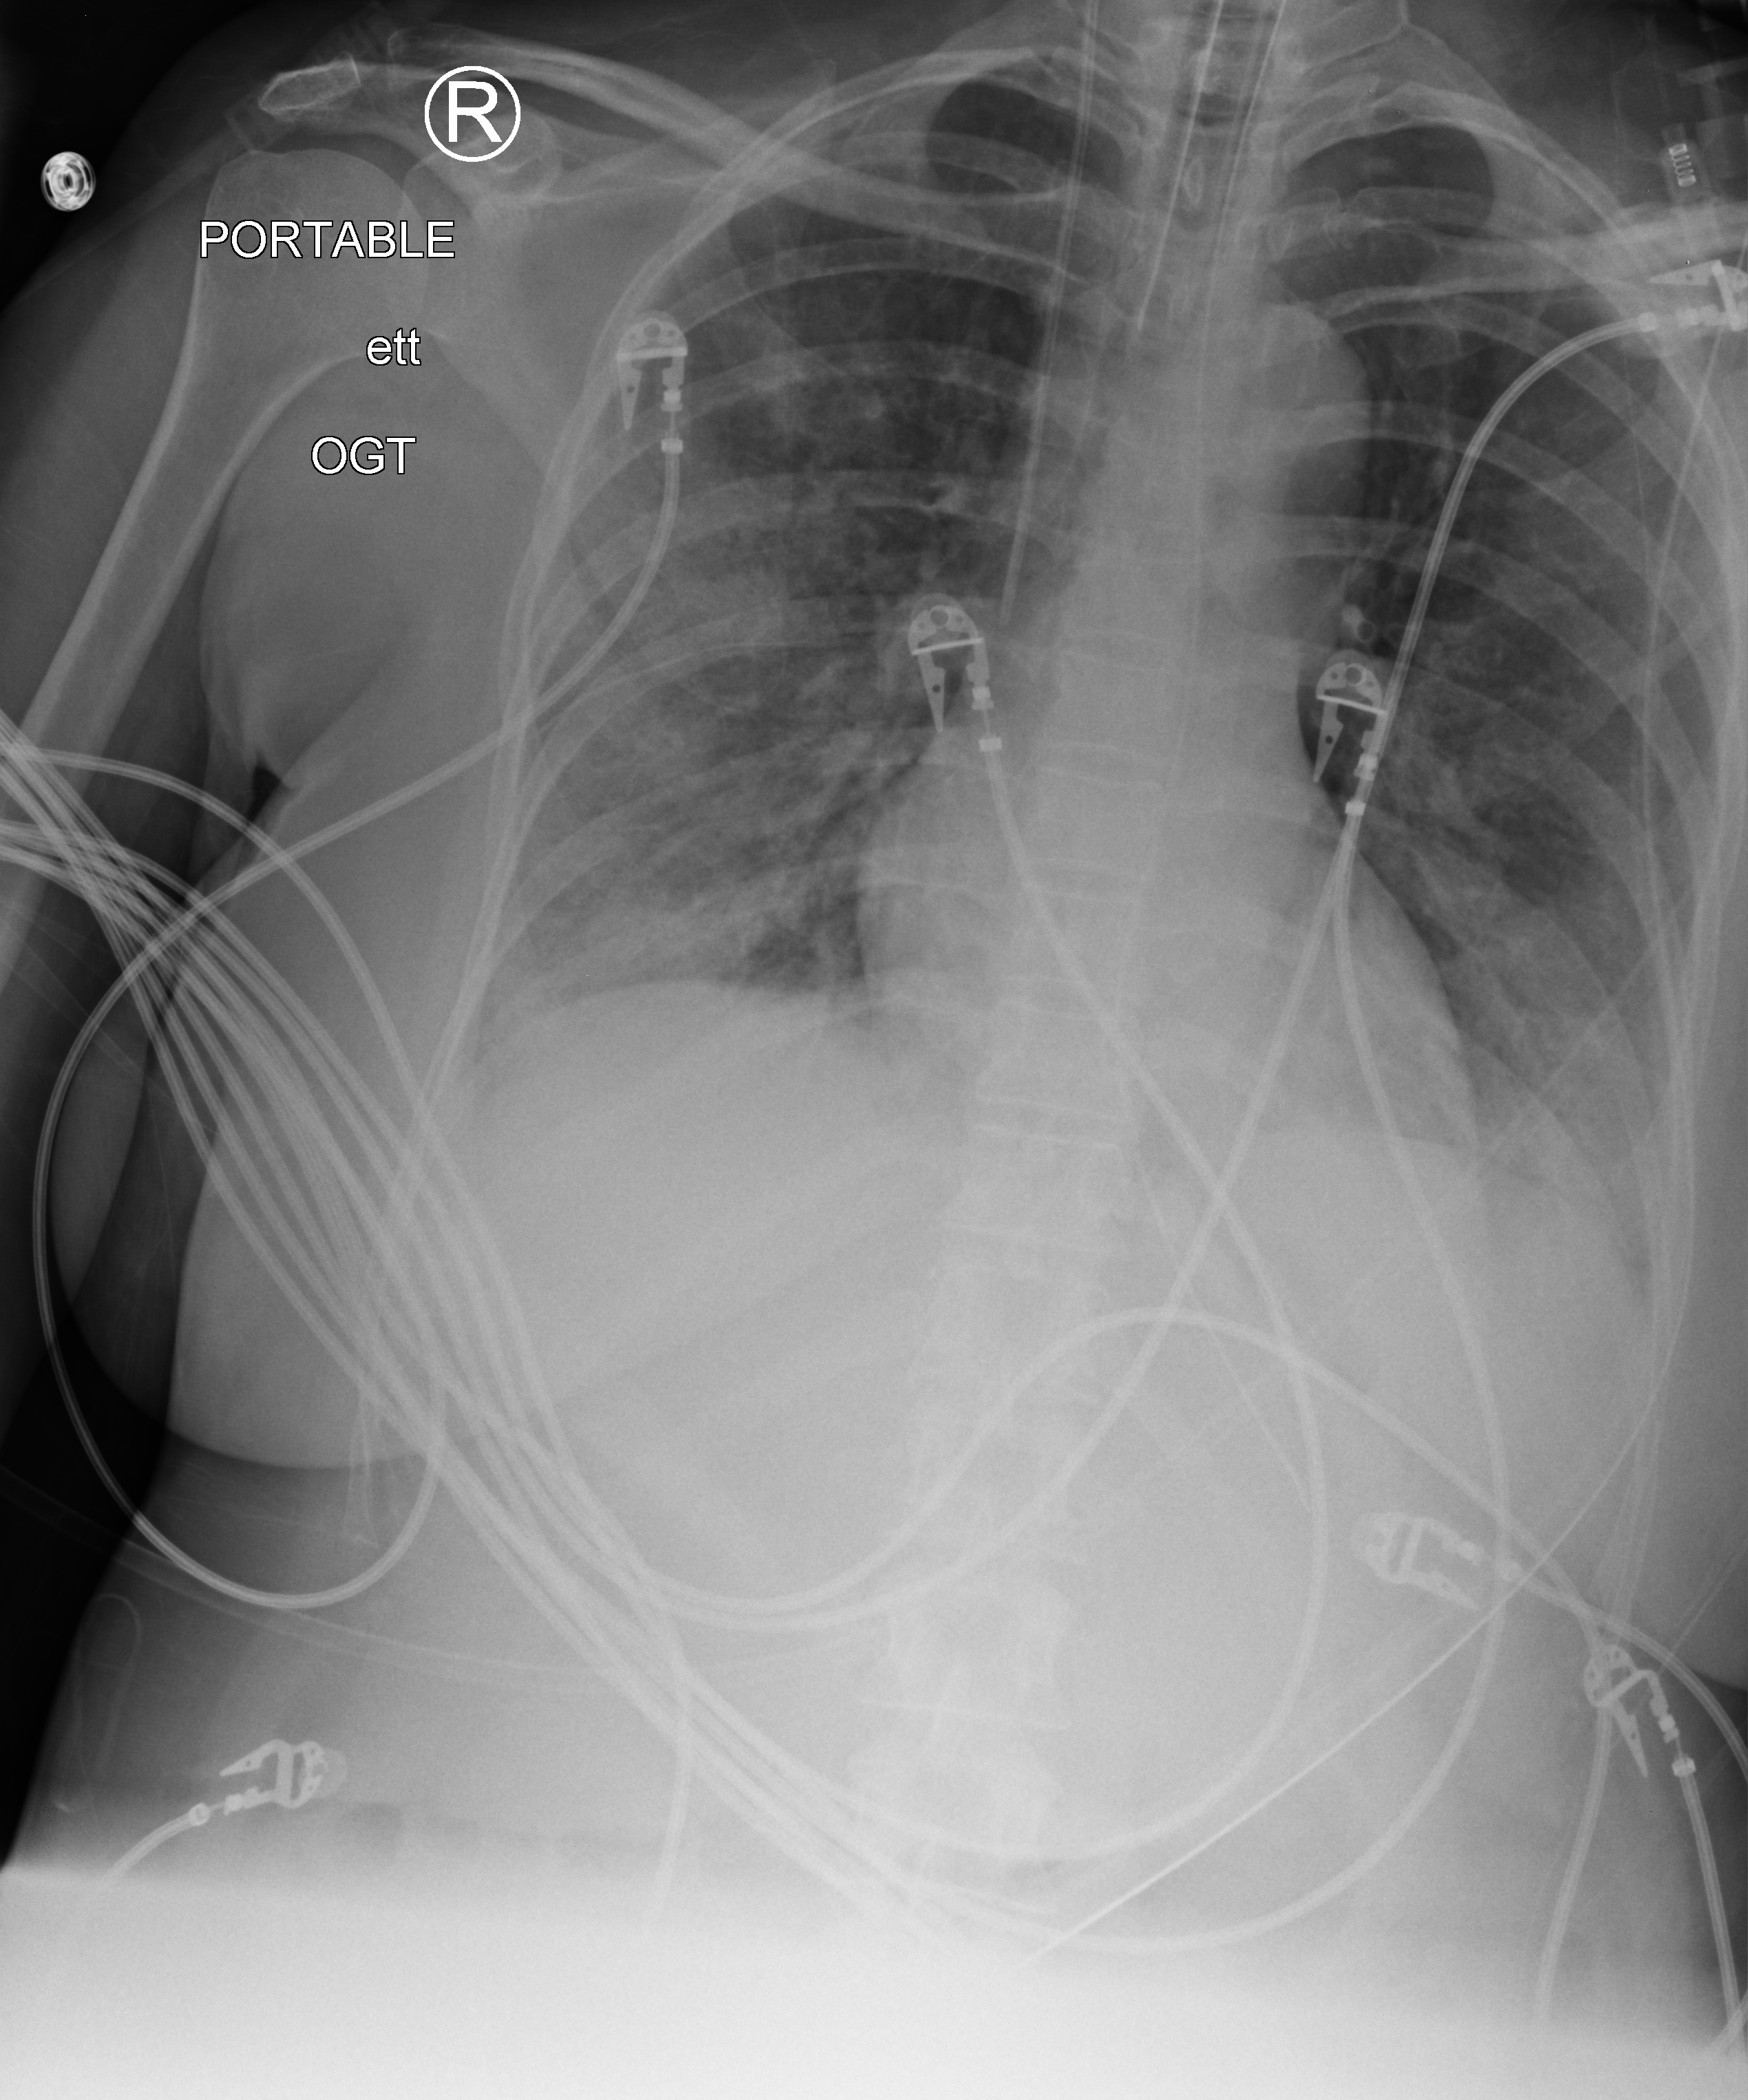
Bedside chest radiograph (computed radiography). Female patient hospitalised with COVID-19, age 18–59 years.
Hospital-stay facts (about this admission, not read from this image; timing relative to this image not recorded): admitted to intensive care during this hospital stay: yes.